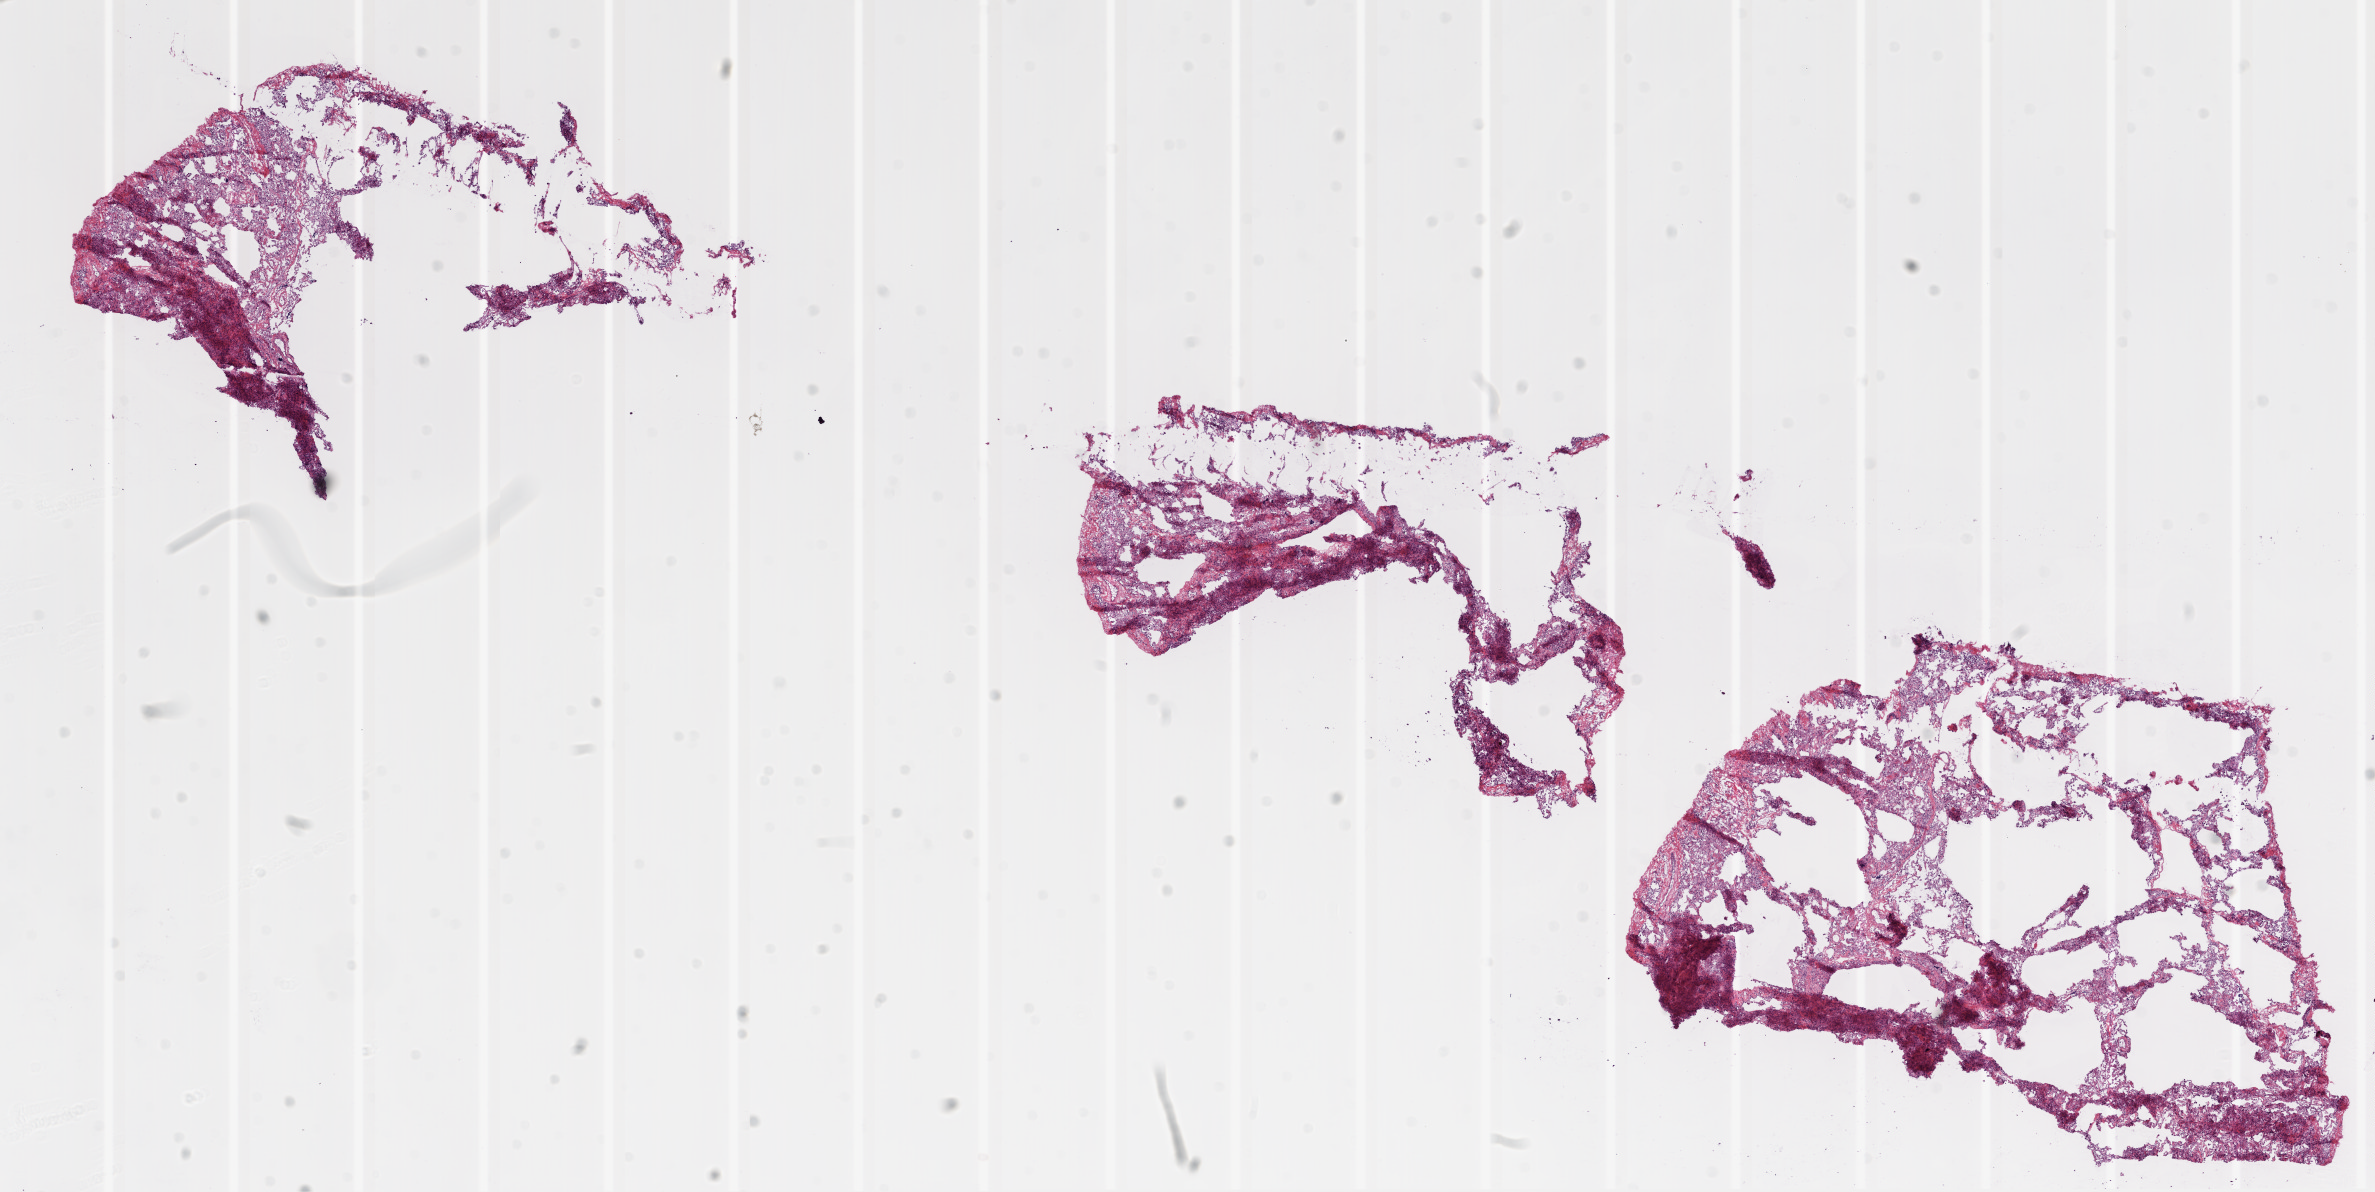
Digitized H&E tissue section (whole slide), a low-resolution overview of the entire scanned area, about 19.1 x 9.6 mm (acquisition: 20x scan); frozen section; solid tissue normal (non-tumour tissue) sample from the lung. Female, age 65 years at initial diagnosis.
This section: solid tissue normal sample (biorepository sample class). Patient diagnosis: Squamous cell carcinoma, NOS (upper lobe, lung).